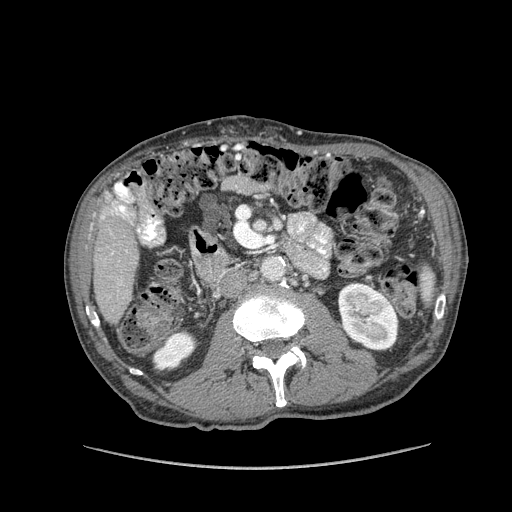
Contrast-enhanced abdominal CT (liver protocol), one axial slice; slice 21 of 162 in the series (ordered by position); reconstruction kernel STANDARD; 100 kVp; soft-tissue window (W 400 / L 40 HU); 512 × 512 image matrix, field of view 400 × 400 mm. Case-level facts recorded for this patient, not image findings: diagnosis: hepatocellular carcinoma (patient treated with transarterial chemoembolisation; whether this scan precedes or follows treatment is not stated here); TNM stage (as recorded): Stage-IIIA; Child-Pugh class: A; tumour nodularity: multinodular; tumour size: 9.9 cm.
Outlined on this slice (semi-automatic segmentation, software-assisted and operator-edited):
- liver parenchyma outside the tumour (the mass and vessels are separate outlines, so this box may not span the whole liver): bounding box [x1, y1, x2, y2] px = [92, 192, 138, 324]
- liver vessels: [102, 205, 127, 252]